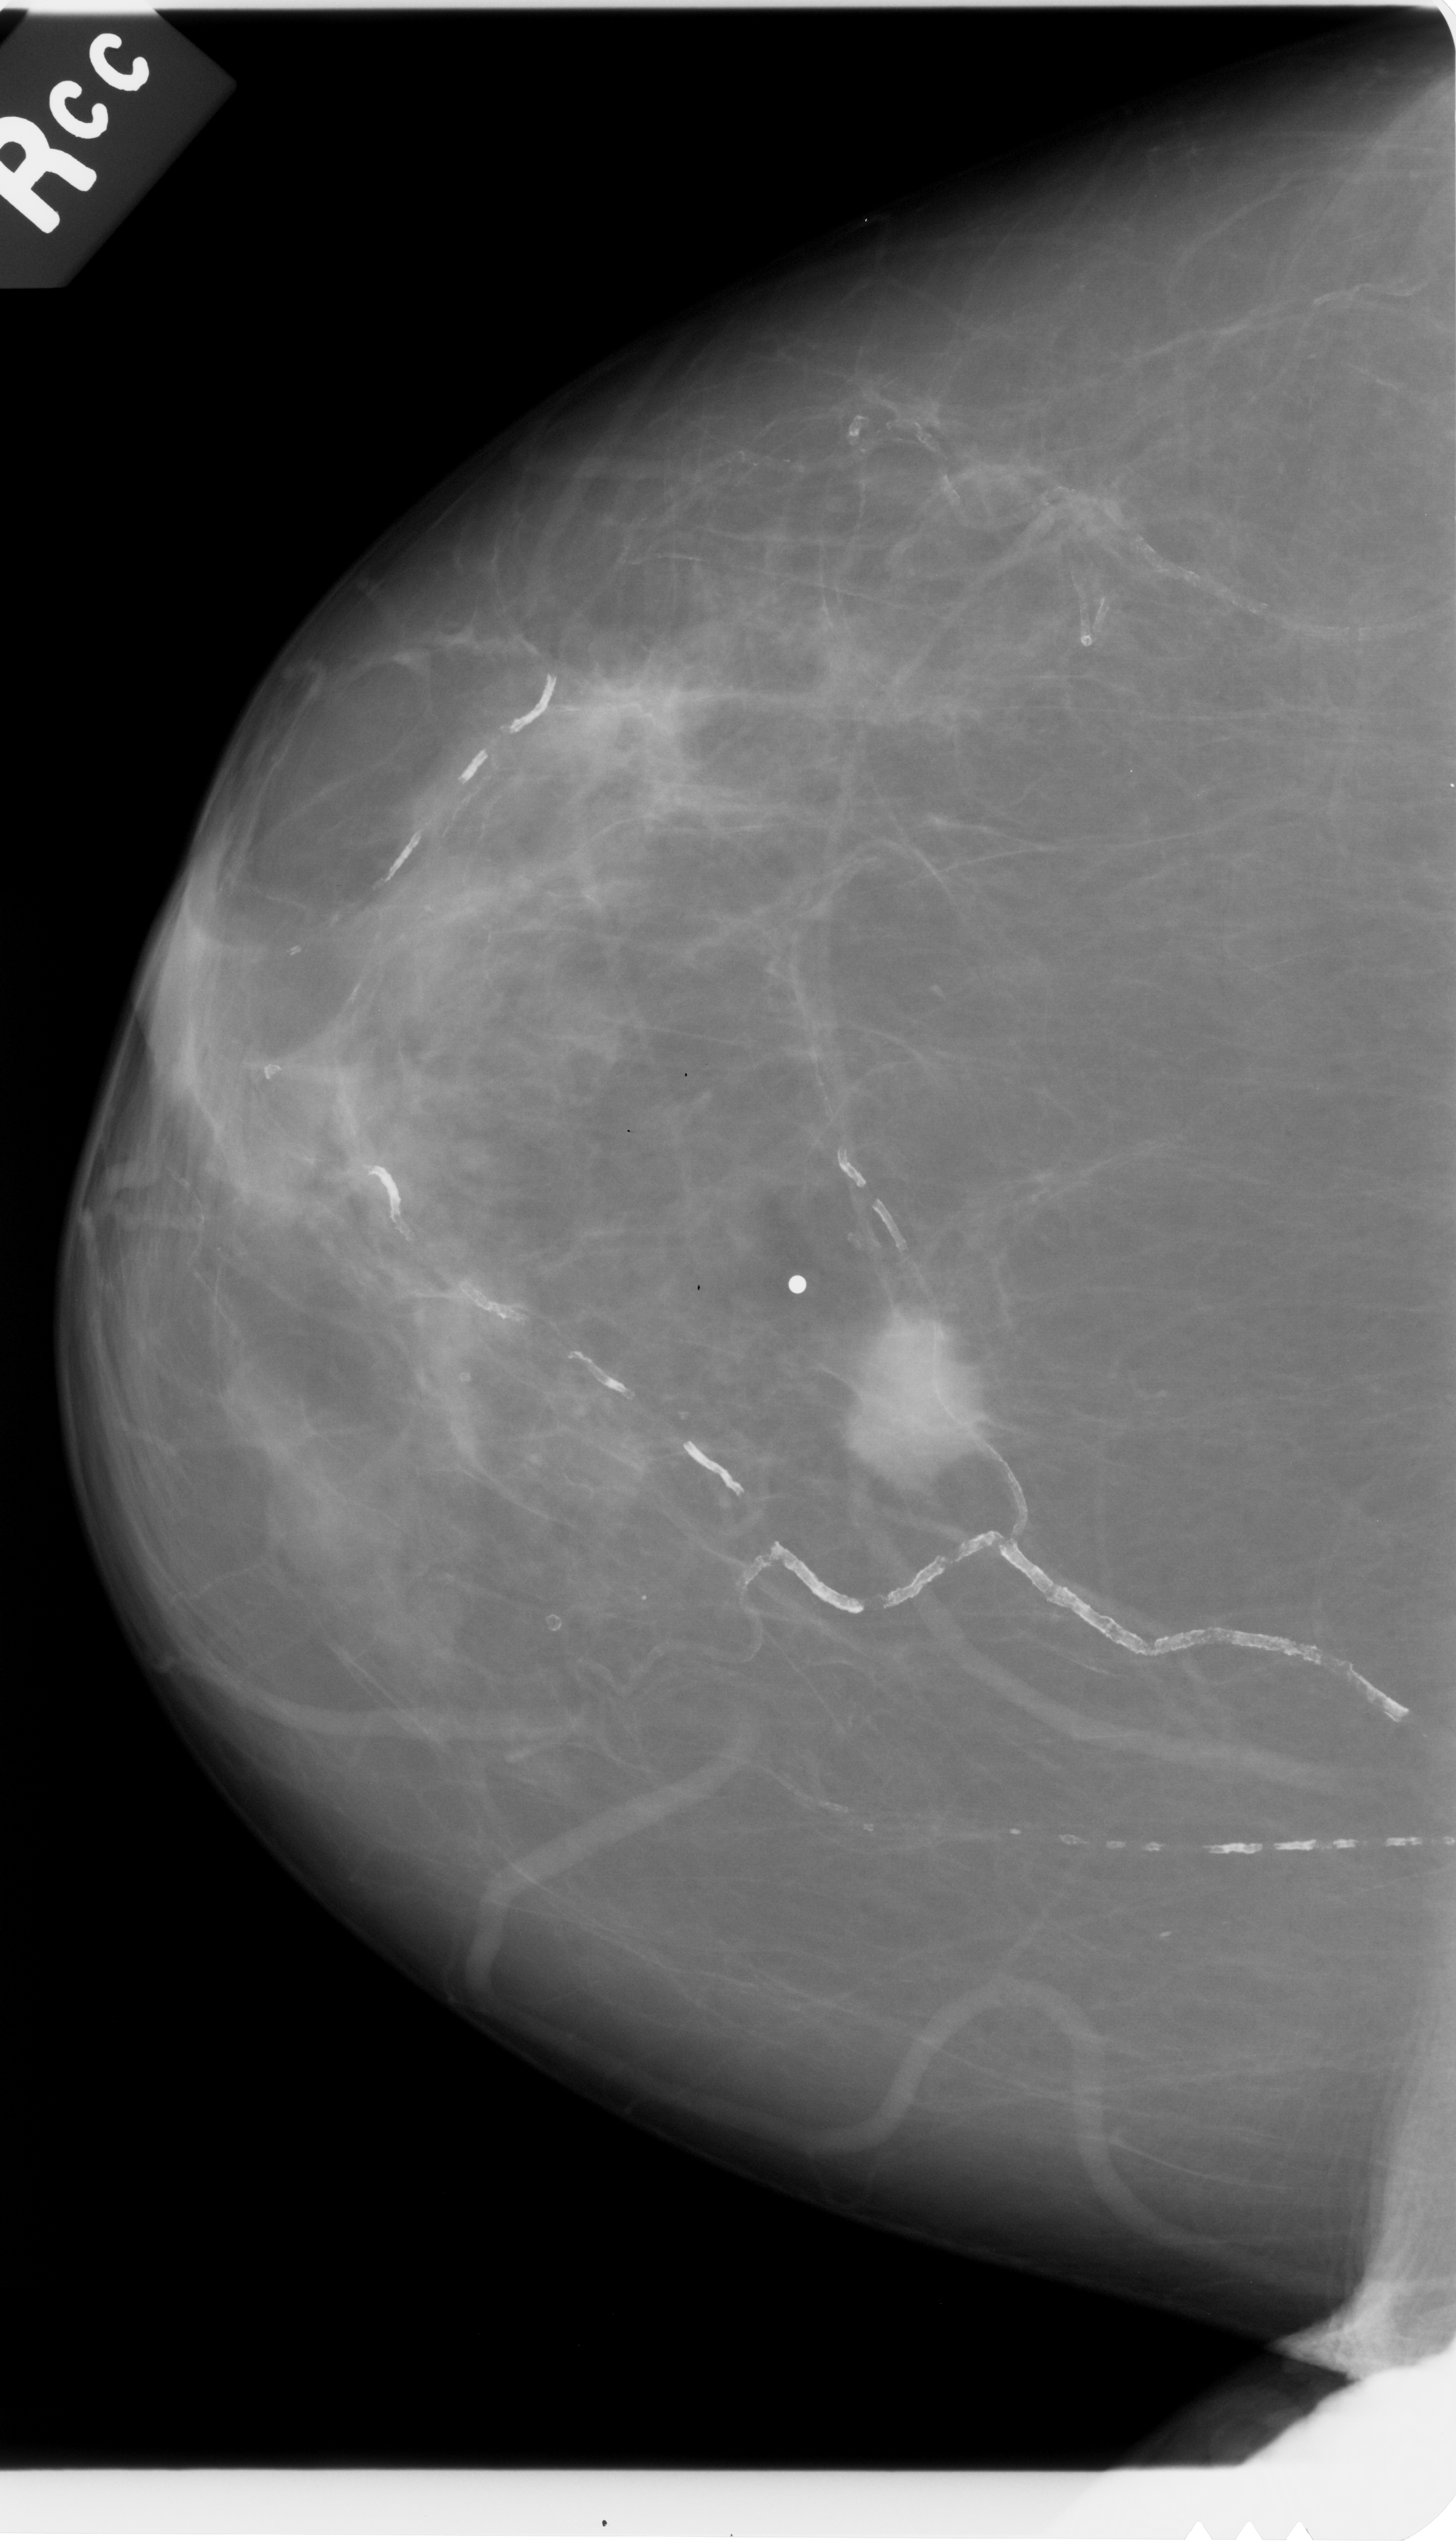
Scanned film-screen mammogram; right breast; CC view; BI-RADS breast density category 1 (scale 1–4); 1456 × 2545 image matrix.
Marked abnormalities (boxes around the expert regions of interest):
- mass, shape irregular, margins spiculated; BI-RADS assessment category 5; pathology result (as recorded, not read from the image): malignant: bounding box (x1, y1, x2, y2) in pixels: (831, 1309, 1008, 1499)